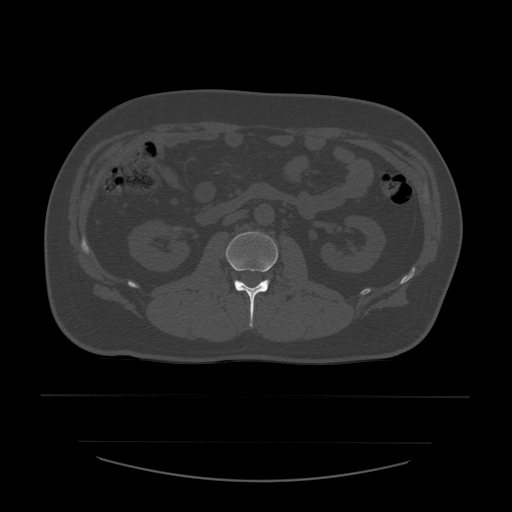
CT including the spine, one axial slice. Position 197 of 532 along the scan axis. Reconstruction kernel STANDARD. 120 kVp. Bone window (W 1800 / L 400 HU). 512 × 512 image matrix, field of view 441 × 441 mm. Patient age 44 years. Case-level facts recorded for this patient, not image findings: primary cancer: soft tissue sarcoma.
Annotated regions visible in this slice (semi-automatic segmentation, software-assisted and operator-edited):
- L2 vertebra: bounding box [x1, y1, x2, y2] px = [226, 232, 278, 327]